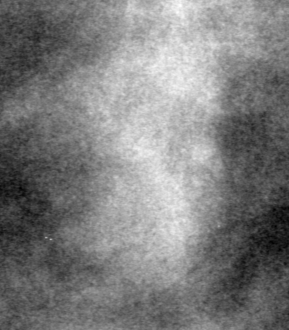
Crop from a digitized film mammogram around one marked abnormality; left breast; CC view.
- Marked abnormality: mass, shape oval, margins obscured; BI-RADS assessment category 0 (incomplete: needs additional imaging); pathology (as recorded): benign.